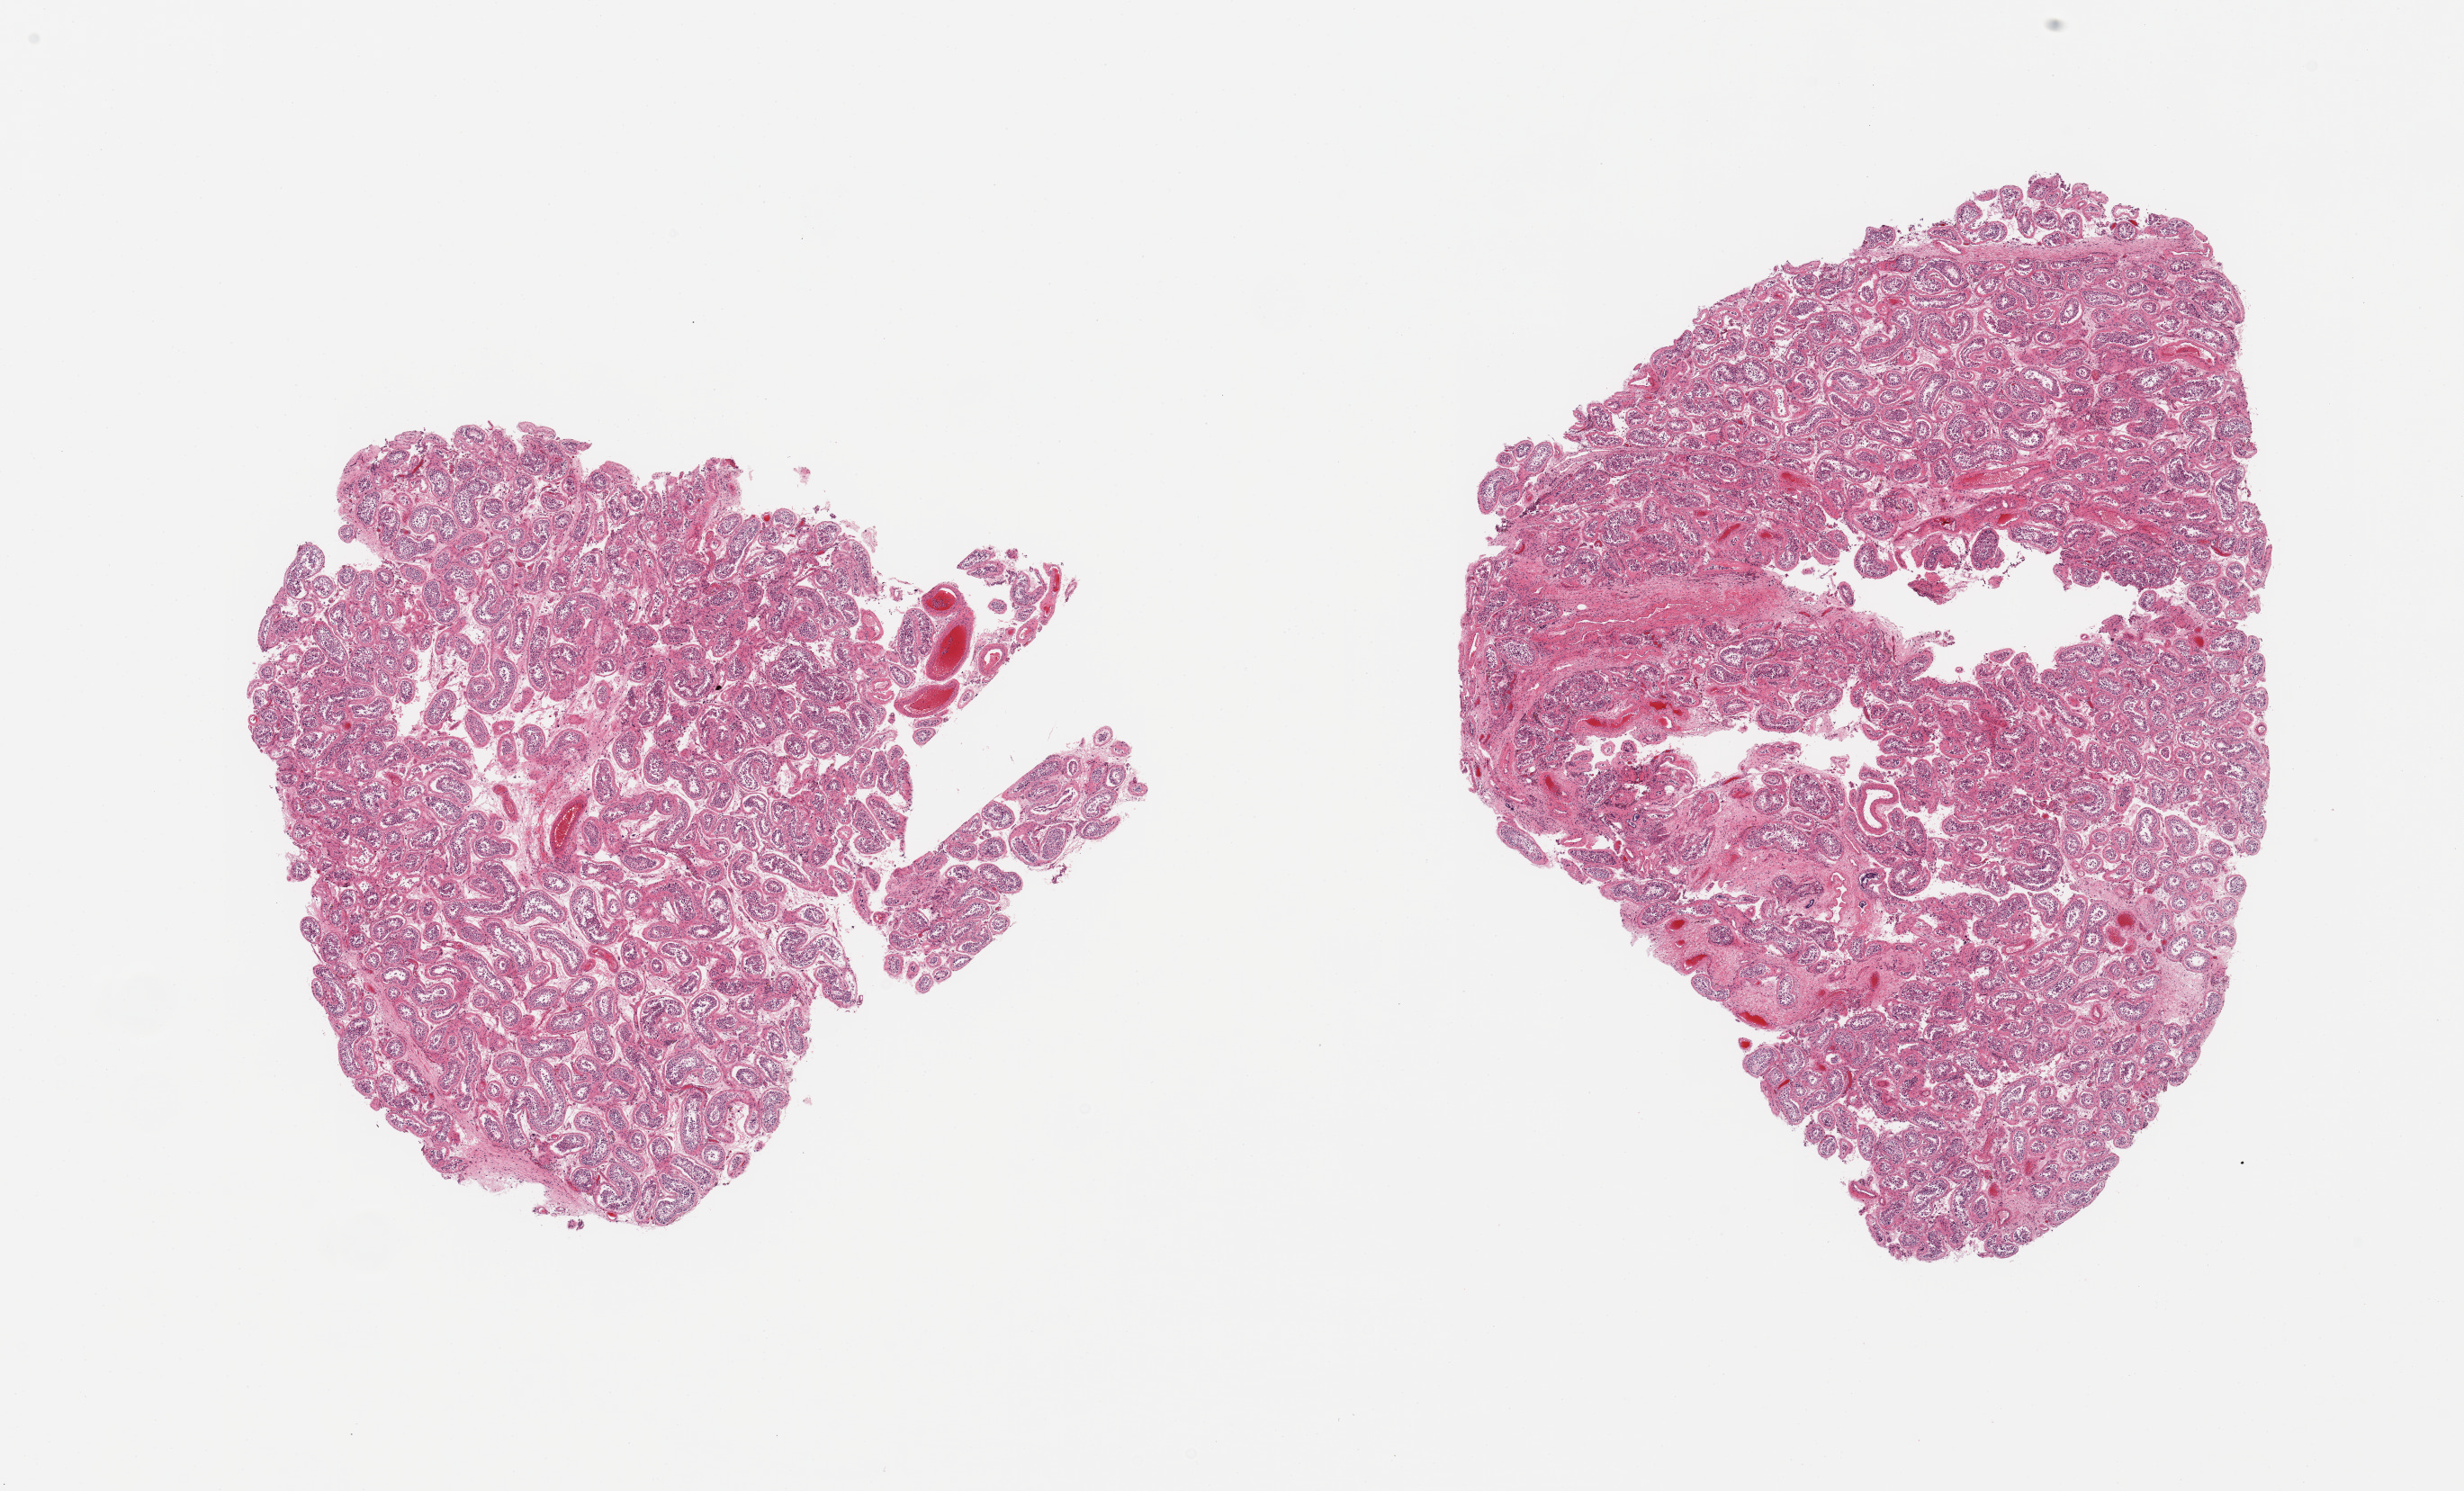
Whole-slide image, H&E stain — shown as a low-resolution overview of the whole scanned area (about 21.7 x 13.1 mm); PAXgene-fixed paraffin-embedded (PFPE) section; sampled site (target tissue): testis; tissue donor sample. Donor sex: male.
• pathologist's review note for this sample: 2 pieces, spermatogenesis substantially reduced